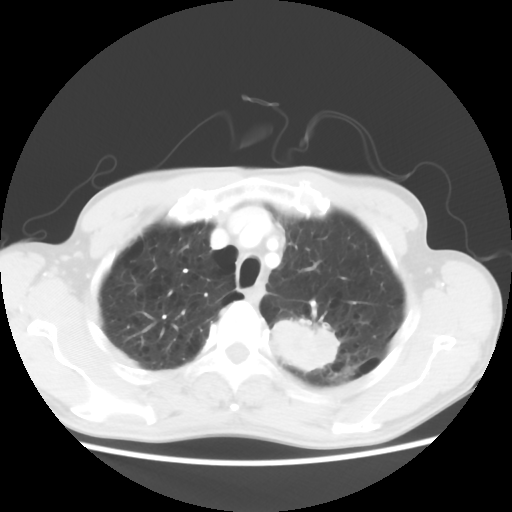
Chest CT, one axial slice. Slice 52 of 64 in the series (ordered by position). Lung window (W 1500 / L -600 HU). 512 × 512 image matrix. Male patient, age 63 years. Case-level facts recorded for this patient, not image findings: clinical TNM (as recorded): T2 N0 M0.
Outlined on this slice (rectangle marked by the reading radiologist):
- lung tumour (recorded histology: adenocarcinoma): bounding box <263,318,345,376> (left, top, right, bottom; pixels)